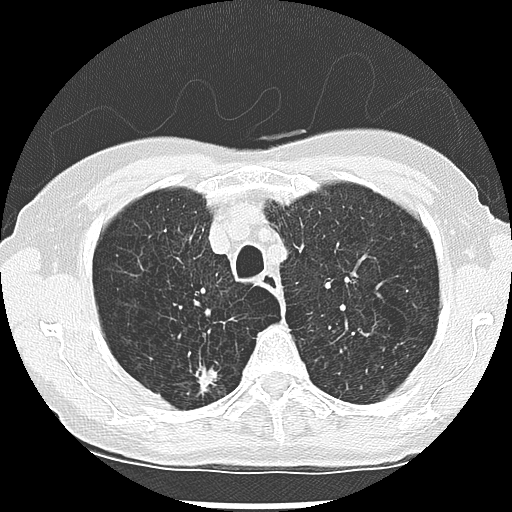
Low-dose screening chest CT, one axial slice. Position 216 of 265 along the scan axis. 120 kVp. Lung window (W 1500 / L -600 HU). 2.5 mm slice thickness. 512 × 512 image matrix, field of view 300 × 300 mm.
Structures marked on this image (outlined manually by an expert reader):
- lesion 1 (nodule, upper lobe of right lung): bounding box (x1, y1, x2, y2) in pixels: (197, 367, 217, 394)